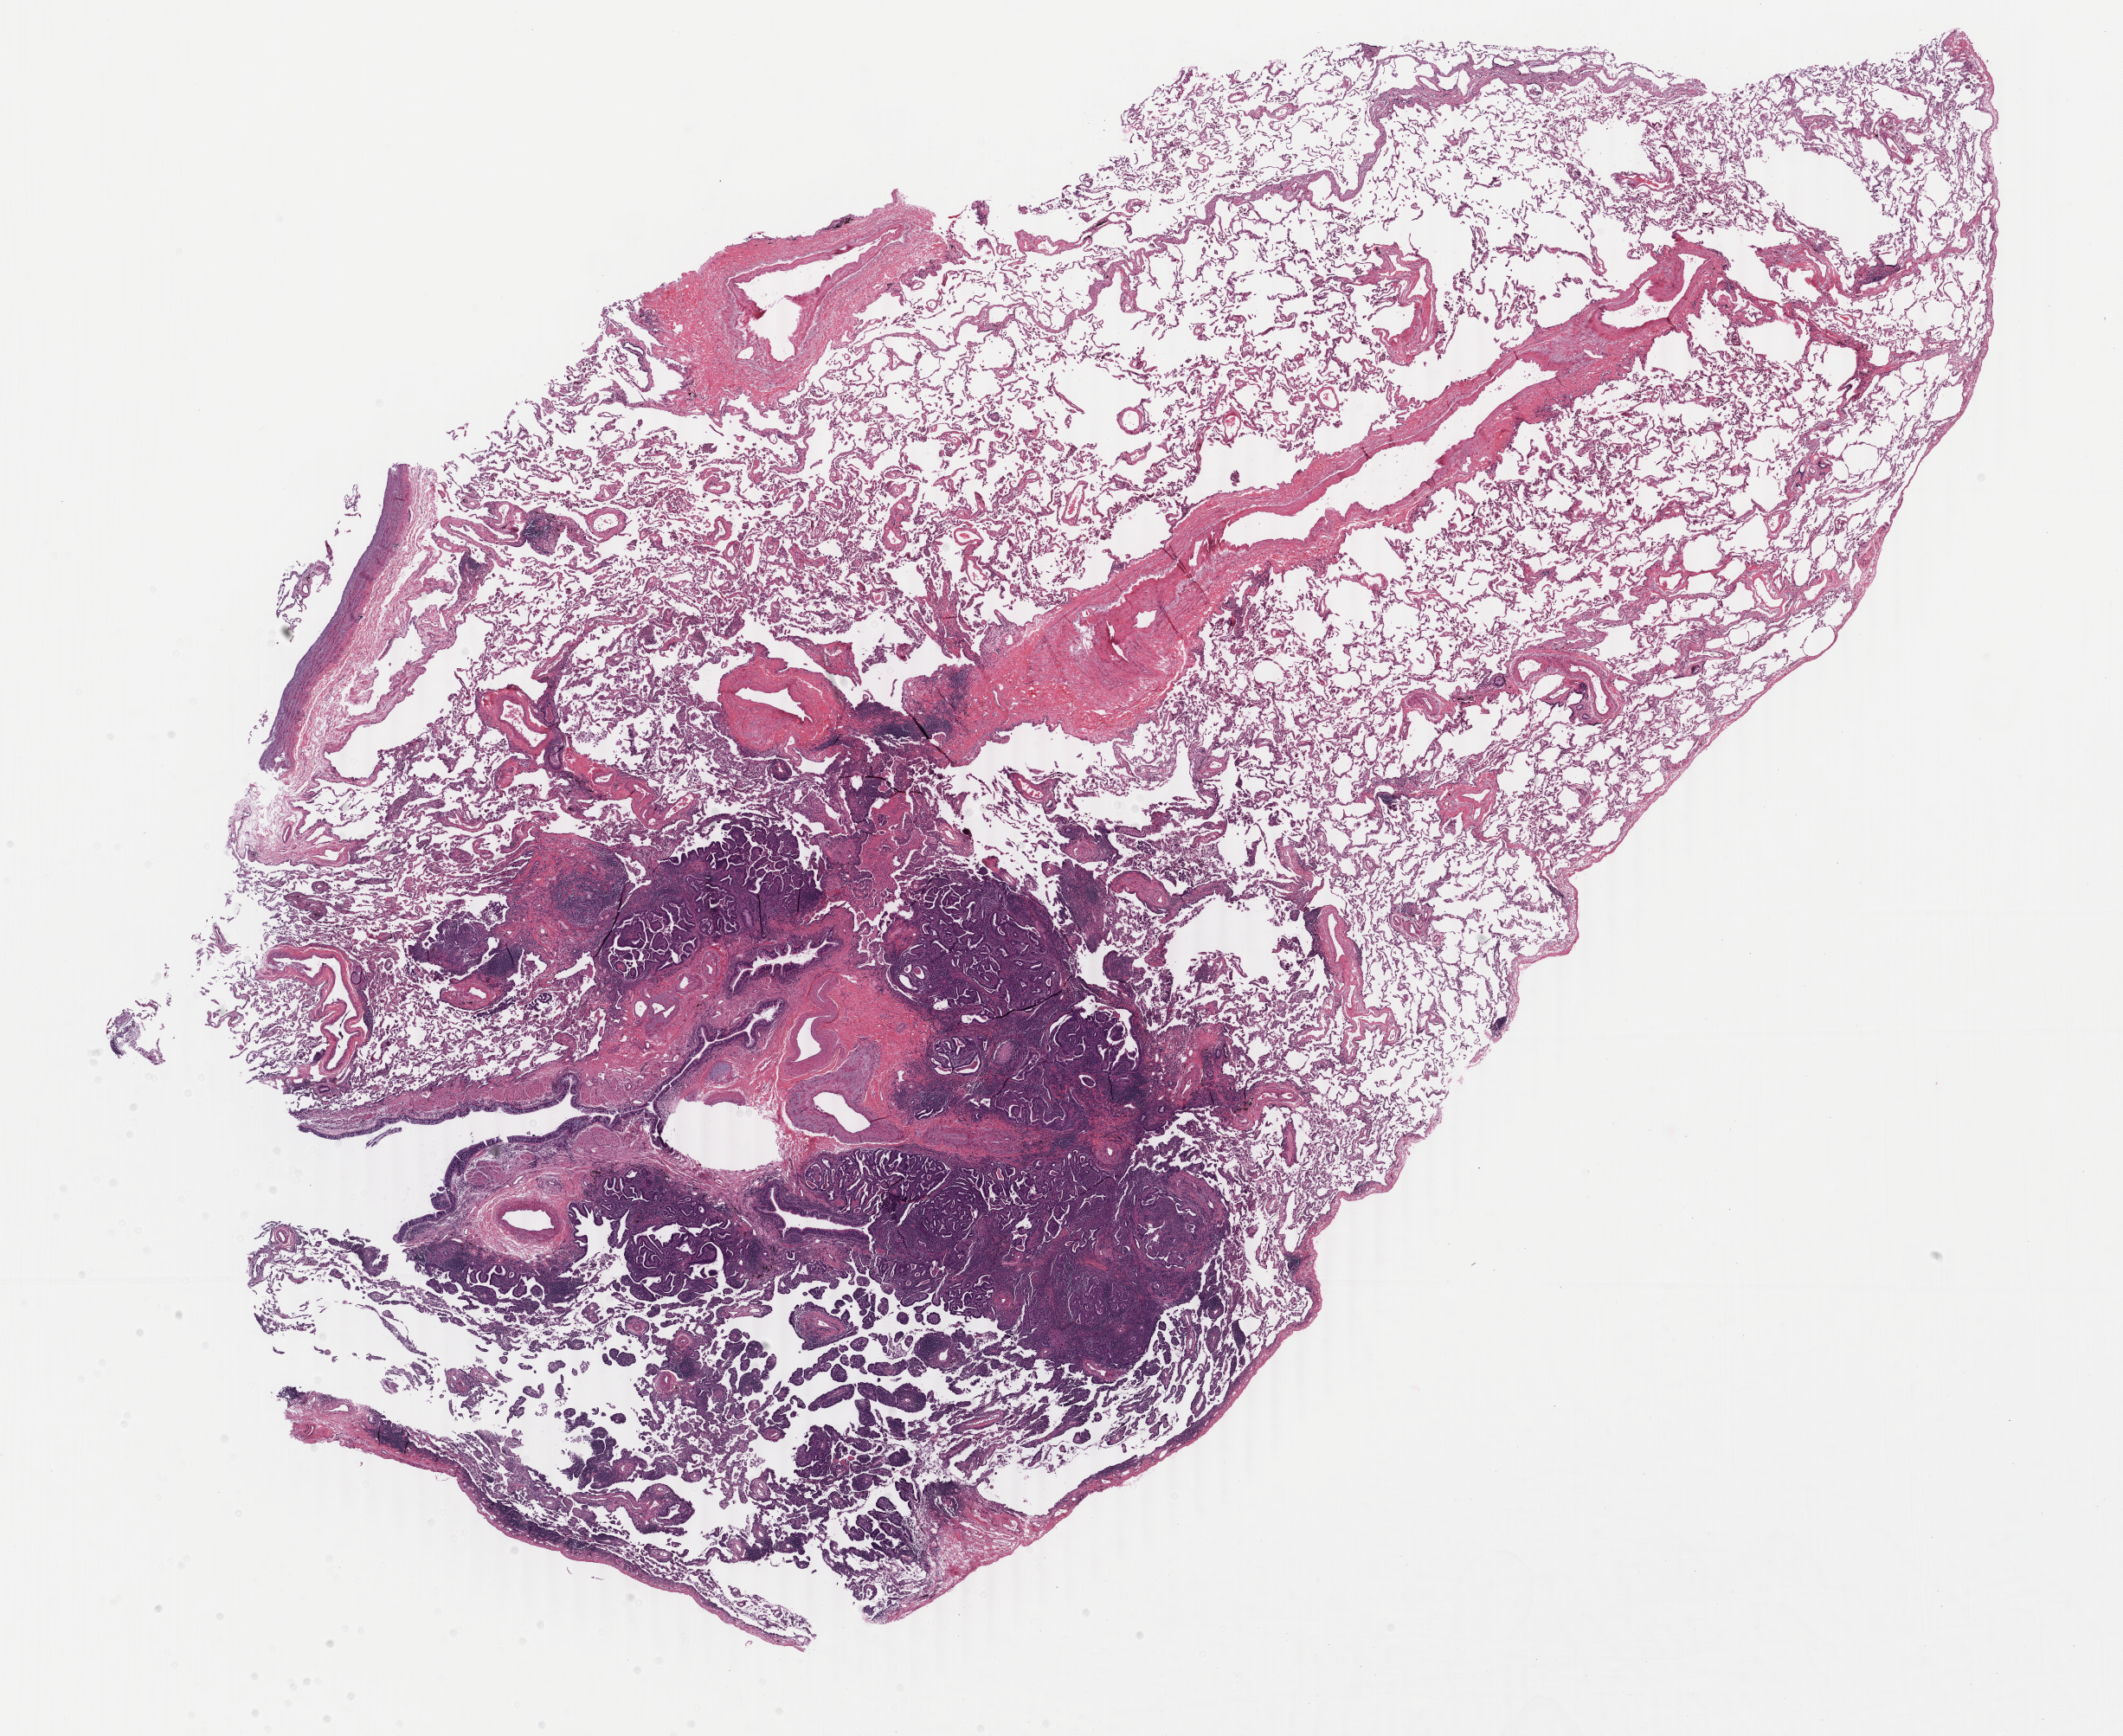
Digitized H&E tissue section (whole slide) — low-resolution overview of the scanned area, about 19.5 x 16.0 mm (acquisition: 40x scan), FFPE section, lung, primary tumour sample. Male, age 66 years at initial diagnosis.
Diagnosis: Adenocarcinoma with mixed subtypes (middle lobe, lung). AJCC pathologic stage: IA.